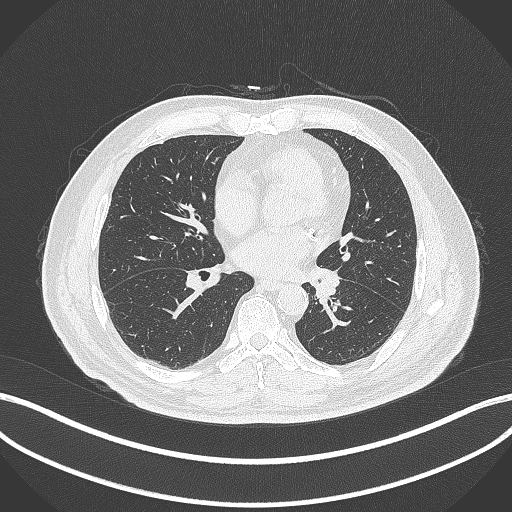
Chest CT, one axial slice; slice 128 of 312 in the series (ordered by position); reconstruction kernel B70f; 120 kVp; lung window (W 1500 / L -600 HU); 1 mm slice thickness; 512 × 512 image matrix, field of view 400 × 400 mm. Patient: male, 71 years. Case-level facts recorded for this patient, not image findings: clinical TNM (as recorded): T1b N0 M0.
Outlined on this slice (bounding box drawn by a radiologist):
- lung tumour (recorded histology: squamous cell carcinoma): bounding box (x1, y1, x2, y2) in pixels: (314, 267, 339, 302)